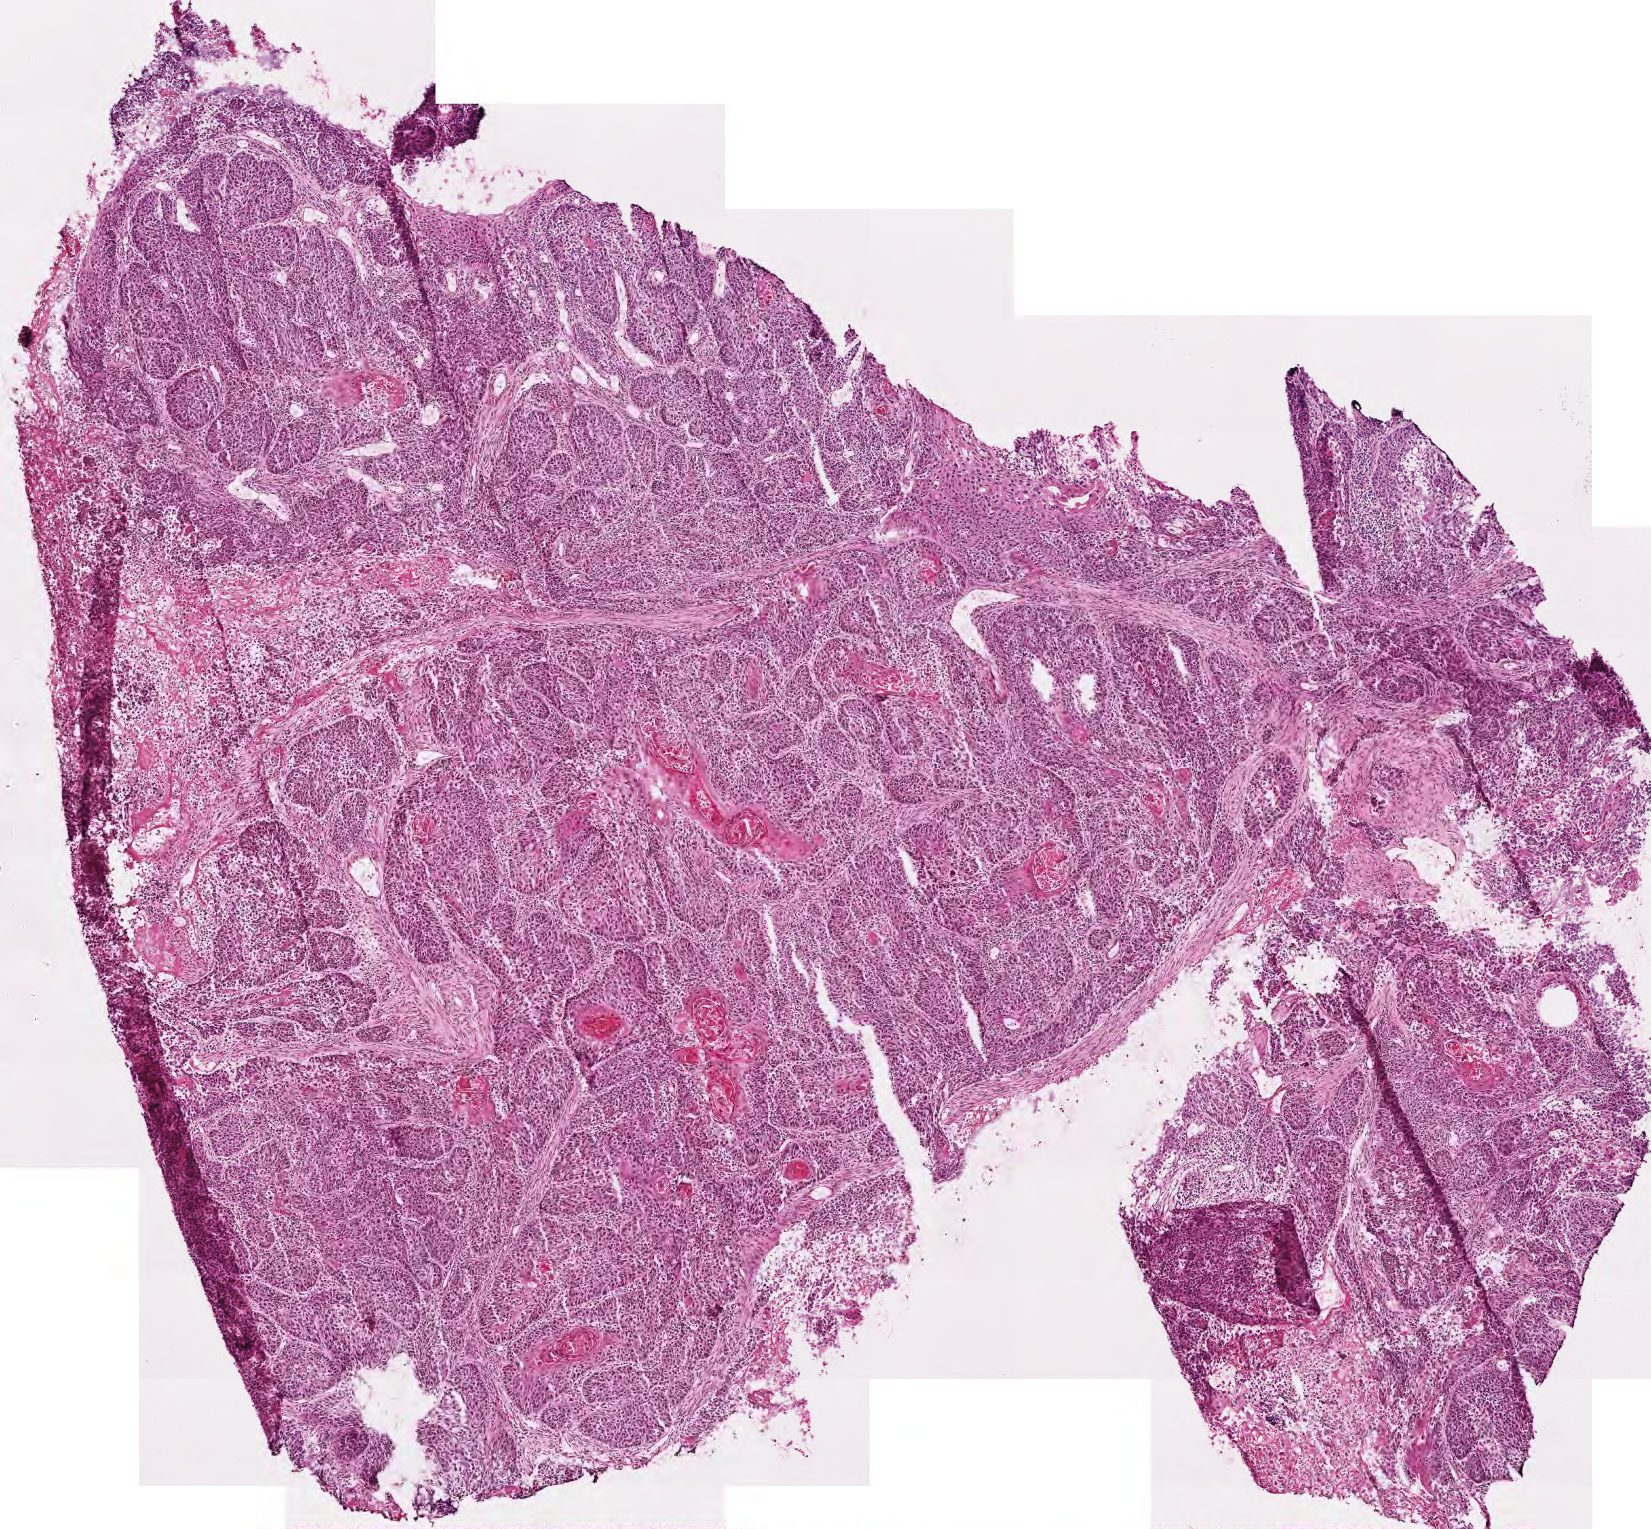
Digitized Hematoxylin and eosin (H&E) stained tissue section (whole slide), a low-resolution overview of the entire scanned area, about 3.3 x 3.1 mm, frozen section from the top of the tissue portion, primary tumour sample from the head and neck. Patient: female, age at initial diagnosis 60 years. Histologic grade: G3 (poorly differentiated). Slide review estimates, as recorded: tumour cells 98%, tumour nuclei 65%, normal cells 0%, stromal cells 0%, necrosis 2%. Infiltration values recorded for this section: lymphocyte infiltration 25%, monocyte infiltration 0%, neutrophil infiltration 0%.
- diagnosis: Squamous cell carcinoma, NOS (larynx, NOS)
- AJCC pathologic stage: IVA (6th edition)